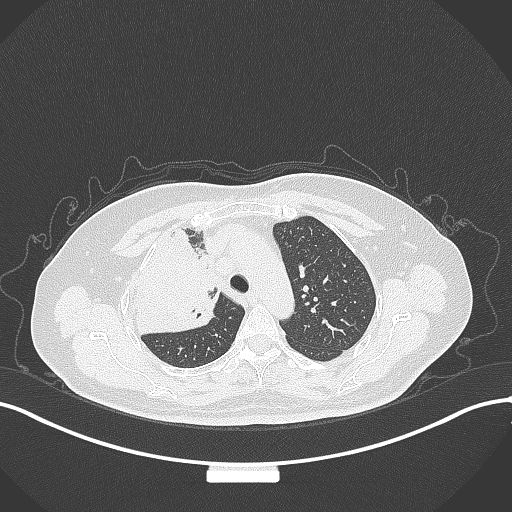
Chest CT, one axial slice; slice 233 of 309 in the series (ordered by position); 120 kVp; lung window (W 1500 / L -600 HU); 1 mm slice thickness; 512 × 512 image matrix, field of view 400 × 400 mm. Female patient, age 60 years. From the clinical record (not read from this slice): clinical TNM (as recorded): T3 N1 M1.
Outlined on this slice (bounding box drawn by a radiologist):
- lung tumour (recorded histology: adenocarcinoma): bounding box (x1, y1, x2, y2) in pixels: (132, 227, 223, 336)